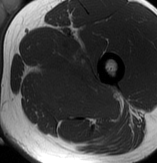
MRI of an extremity soft-tissue mass, one axial slice; slice 55 of 70 in the series (ordered by position); MR volume resampled by the dataset authors to the PET/CT grid (not the native acquisition matrix); 157 × 163 image matrix, field of view 153 × 159 mm. Male patient. From the clinical record (not read from this slice): histological type: extraskeletal osteosarcoma; grade: high; site of the primary tumour: left adductur.
Outlined on this slice (expert contour drawn on MRI and transferred to this co-registered scan by the dataset authors):
- gross tumour volume (mass): bounding box <33,49,121,123> (left, top, right, bottom; pixels)